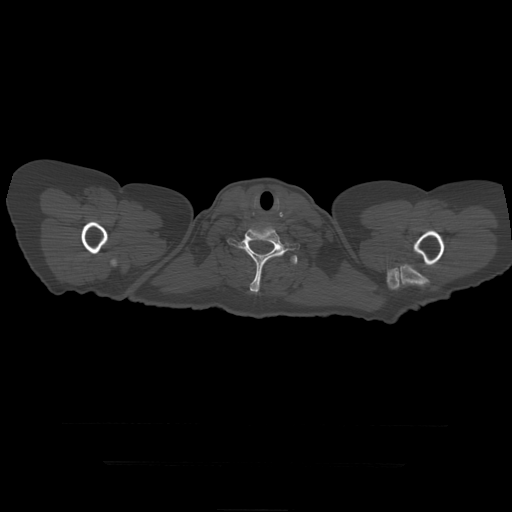
CT including the spine, one axial slice. Position 389 of 399 along the scan axis. Reconstruction kernel STANDARD. 120 kVp. Bone window (W 1800 / L 400 HU). 1.25 mm slice thickness. 512 × 512 image matrix, field of view 450 × 450 mm. Patient age 41 years. Case-level facts recorded for this patient, not image findings: primary cancer: breast.
Annotated regions visible in this slice (semi-automatically segmented with operator editing):
- T1 vertebra: bounding box <228,227,300,294> (left, top, right, bottom; pixels)
- T2 vertebra: <291,255,298,265>